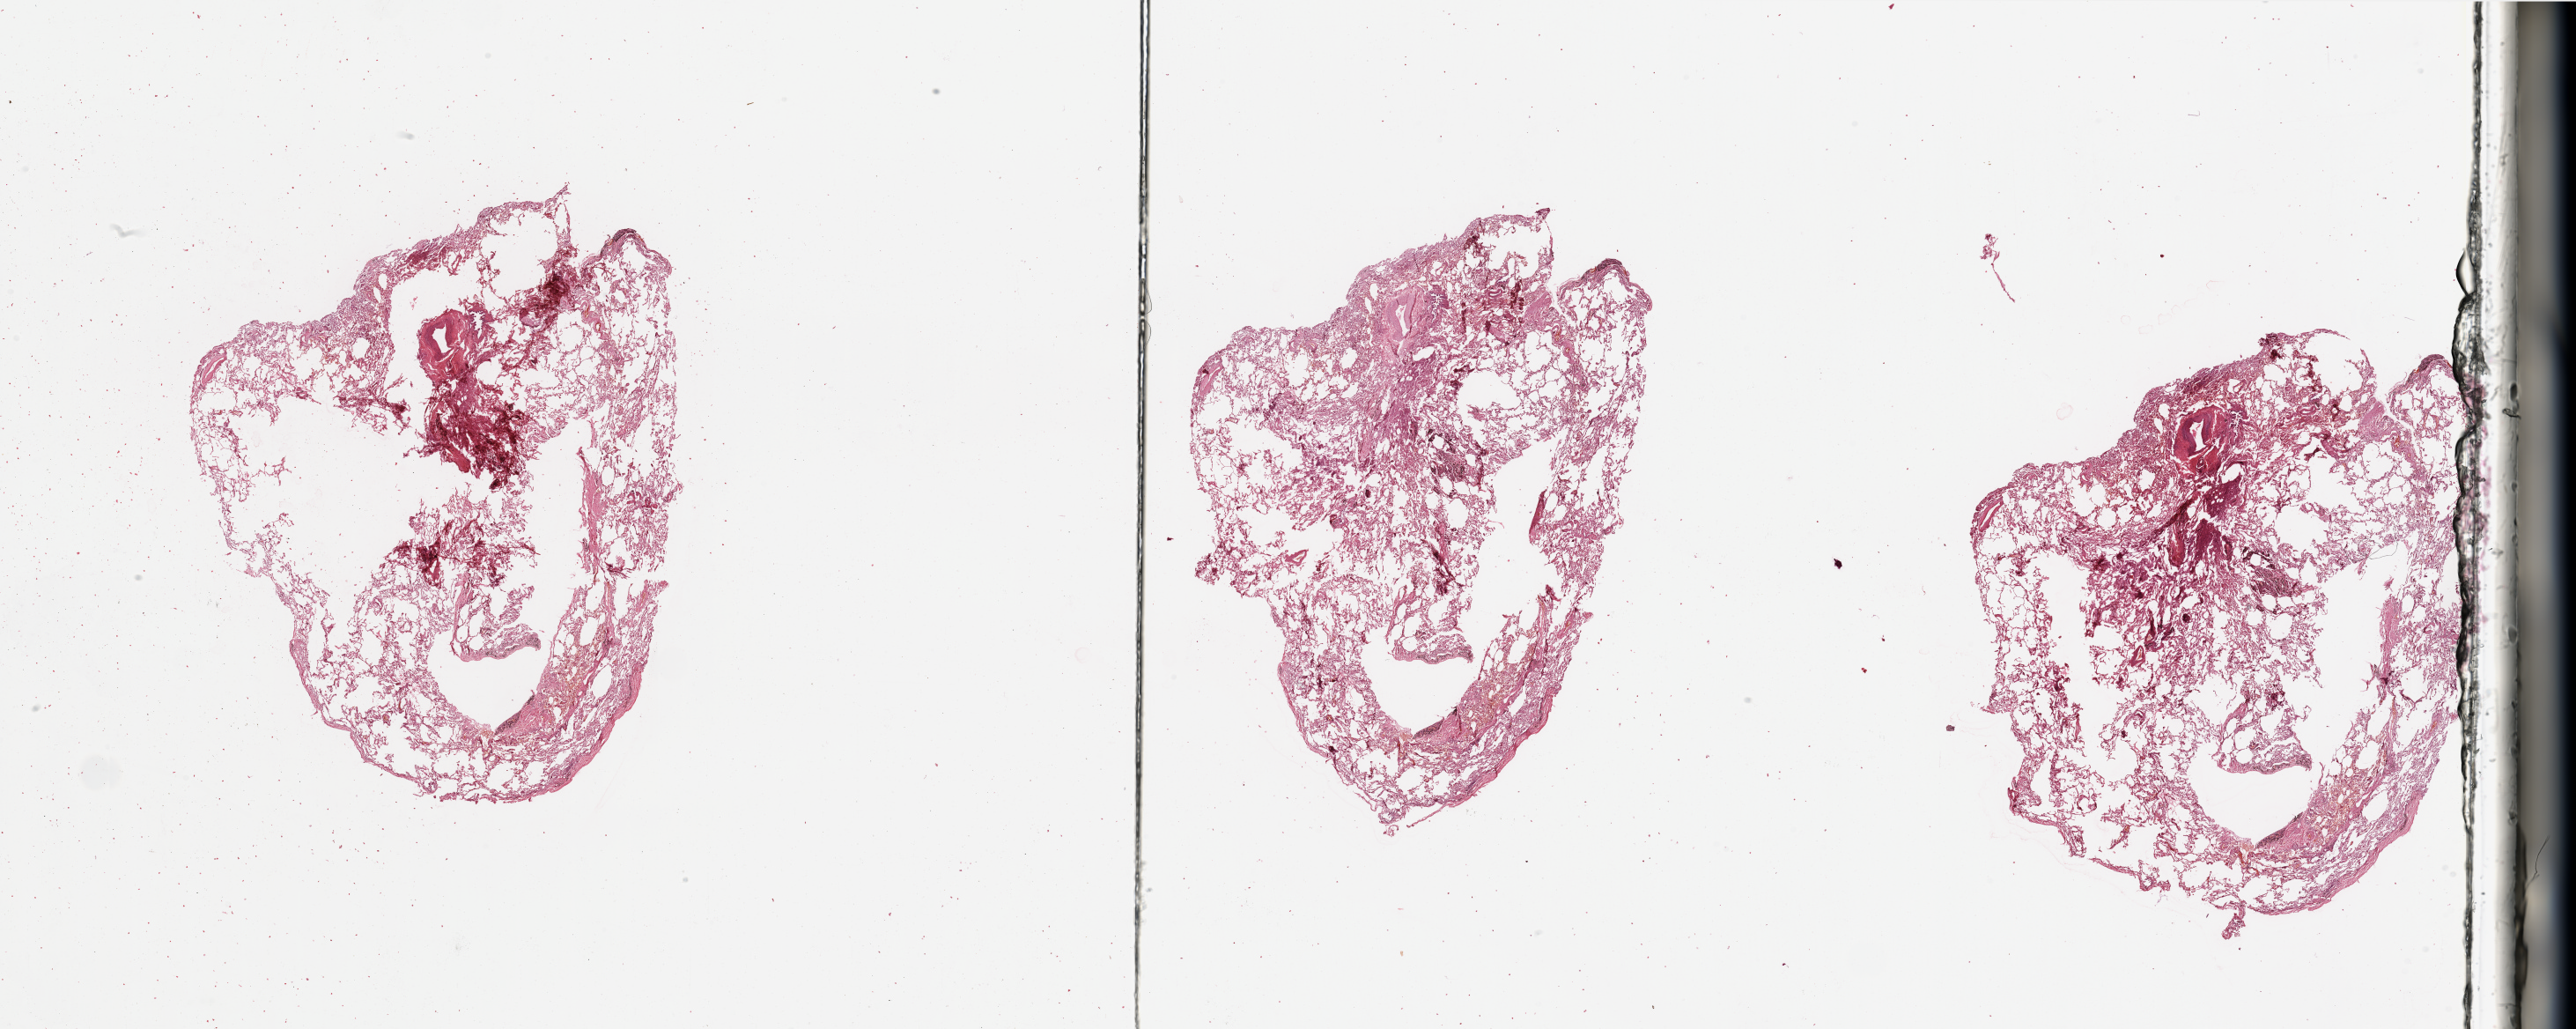
Digitized Hematoxylin and eosin (H&E) stained tissue section (whole slide), a low-resolution overview of the entire scanned area, about 46.3 x 18.5 mm; lung, normal (non-tumour) tissue. 66-year-old male patient.
This section: normal (non-tumour) tissue from the same patient. Patient diagnosis (cohort enrolment): squamous cell carcinoma (lung).